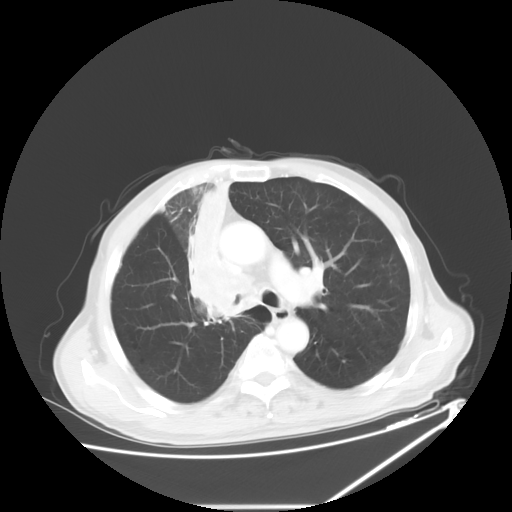
Chest CT, one axial slice; position 40 of 60 along the scan axis; reconstruction kernel STANDARD; 120 kVp; lung window (W 1500 / L -600 HU); 5 mm slice thickness; 512 × 512 image matrix. Patient: male, 73 years. Case-level facts recorded for this patient, not image findings: clinical TNM (as recorded): T2a N1 M0.
Annotated regions visible in this slice (bounding box drawn by a radiologist):
- lung tumour (recorded histology: squamous cell carcinoma): bounding box [x1, y1, x2, y2] px = [184, 180, 252, 324]